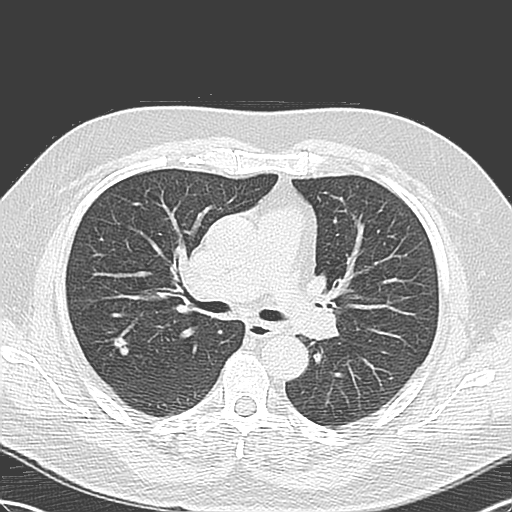
Low-dose screening chest CT, one axial slice. Position 73 of 131 along the scan axis. 120 kVp. Lung window (W 1500 / L -600 HU). 512 × 512 image matrix.
Annotated regions visible in this slice (outlined manually by an expert reader):
- lesion 1 (tumor, upper lobe of right lung): bounding box <113,337,129,356> (left, top, right, bottom; pixels)